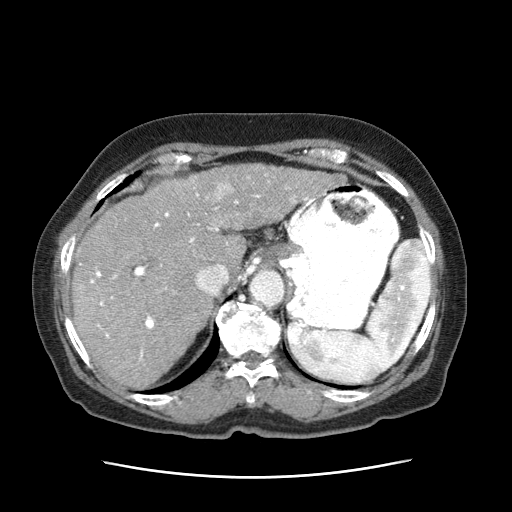
Contrast-enhanced abdominal CT (liver protocol), one axial slice. Slice 48 of 63 in the series (ordered by position). Reconstruction kernel STANDARD. 120 kVp. Intravenous contrast given. Soft-tissue window (W 400 / L 40 HU). 2.5 mm slice thickness. 512 × 512 image matrix, field of view 360 × 360 mm. Patient: female, 79 years. From the clinical record (not read from this slice): diagnosis: hepatocellular carcinoma (patient treated with transarterial chemoembolisation; whether this scan precedes or follows treatment is not stated here); TNM stage (as recorded): Stage-II; Child-Pugh class: B; tumour differentiation: well differentiated; tumour nodularity: multinodular.
Annotated regions visible in this slice (semi-automatic segmentation, software-assisted and operator-edited):
- abdominal aorta: bounding box (x1, y1, x2, y2) in pixels: (251, 271, 286, 308)
- liver parenchyma outside the tumour (the mass and vessels are separate outlines, so this box may not span the whole liver): (72, 178, 248, 391)
- mass: (188, 165, 347, 230)
- liver vessels: (89, 187, 297, 361)